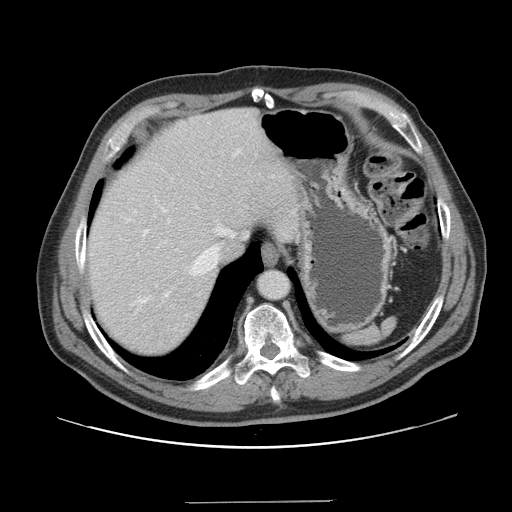
Contrast-enhanced abdominal CT, one axial slice; slice 129 of 151 in the series (ordered by position); intravenous contrast given; soft-tissue window (W 400 / L 40 HU); 2.5 mm slice thickness; 512 × 512 image matrix. Male patient, age 63 years. Case-level facts recorded for this patient, not image findings: diagnosis: colorectal cancer liver metastases, imaged before liver resection; multiple liver metastases: no; largest metastasis: 2.1 cm; disease in both lobes: no.
Annotated regions visible in this slice (manually delineated by an expert):
- hepatic veins: bounding box (x1, y1, x2, y2) in pixels: (129, 151, 239, 302)
- liver: (88, 109, 303, 357)
- planned liver remnant (the part of the liver to remain after resection): (88, 122, 250, 357)